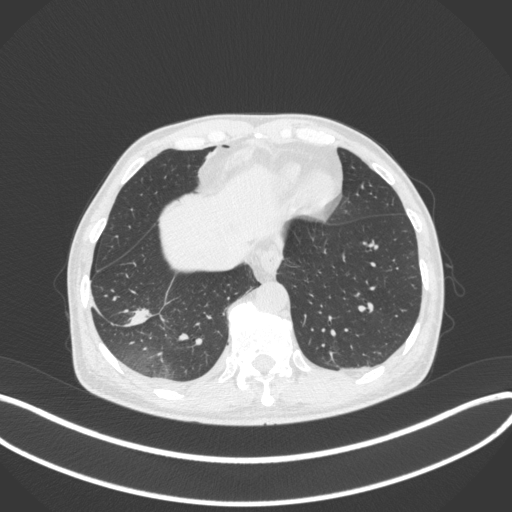
Chest CT, one axial slice; slice 85 of 385 in the series (ordered by position); lung window (W 1500 / L -600 HU); 512 × 512 image matrix, field of view 400 × 400 mm. Male patient, age 64 years. From the clinical record (not read from this slice): clinical TNM (as recorded): T3 N0 M0; histopathological grade: G2-3.
Outlined on this slice (rectangle marked by the reading radiologist):
- lung tumour (recorded histology: adenocarcinoma): bounding box (x1, y1, x2, y2) in pixels: (119, 300, 156, 337)